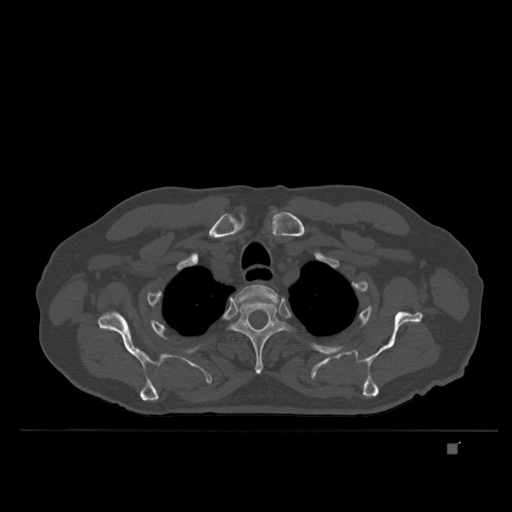
CT including the spine, one axial slice. Position 302 of 435 along the scan axis. Bone window (W 1800 / L 400 HU). 512 × 512 image matrix. Male patient, age 73 years. From the clinical record (not read from this slice): primary cancer: skin.
Outlined on this slice (semi-automatic segmentation, software-assisted and operator-edited):
- T2 vertebra: bounding box (x1, y1, x2, y2) in pixels: (231, 284, 279, 309)
- T3 vertebra: (229, 300, 289, 374)